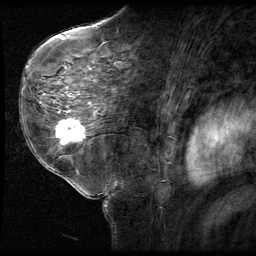
Breast MRI (dynamic contrast-enhanced), one sagittal slice; position 37 of 58 along the scan axis; 3 images stored at this slice position (order not interpretable as contrast timing); 1.5 T; TE 4.2 ms, TR 9 ms; 256 × 256 image matrix, field of view 180 × 180 mm. Female patient, age 58 years. From the clinical record (not read from this slice): setting: breast cancer imaged before/during neoadjuvant chemotherapy; receptor status: HR-positive, HER2-negative.
Structures marked on this image (semi-automatic segmentation, software-assisted and operator-edited):
- analysis volume of interest (the breast-tissue region the enhancement analysis was run in; not a lesion): box from (x=51, y=116) to (x=93, y=151) px
- tumour enhancement mask (voxels above the 140 % enhancement threshold inside the analysis volume of interest): (x=57, y=118)–(x=86, y=143)